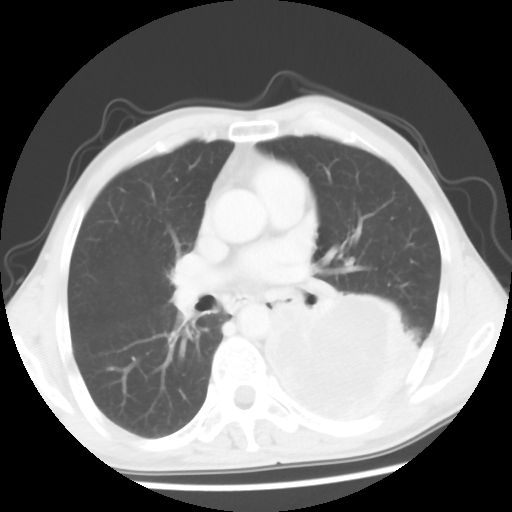
Chest CT, one axial slice. Position 31 of 56 along the scan axis. 120 kVp. Lung window (W 1500 / L -600 HU). 5 mm slice thickness. 512 × 512 image matrix, field of view 318 × 318 mm. Male patient, age 60 years. From the clinical record (not read from this slice): clinical TNM (as recorded): T4 N0 M0.
Structures marked on this image (rectangle marked by the reading radiologist):
- lung tumour (recorded histology: squamous cell carcinoma): bounding box [x1, y1, x2, y2] px = [248, 276, 439, 424]